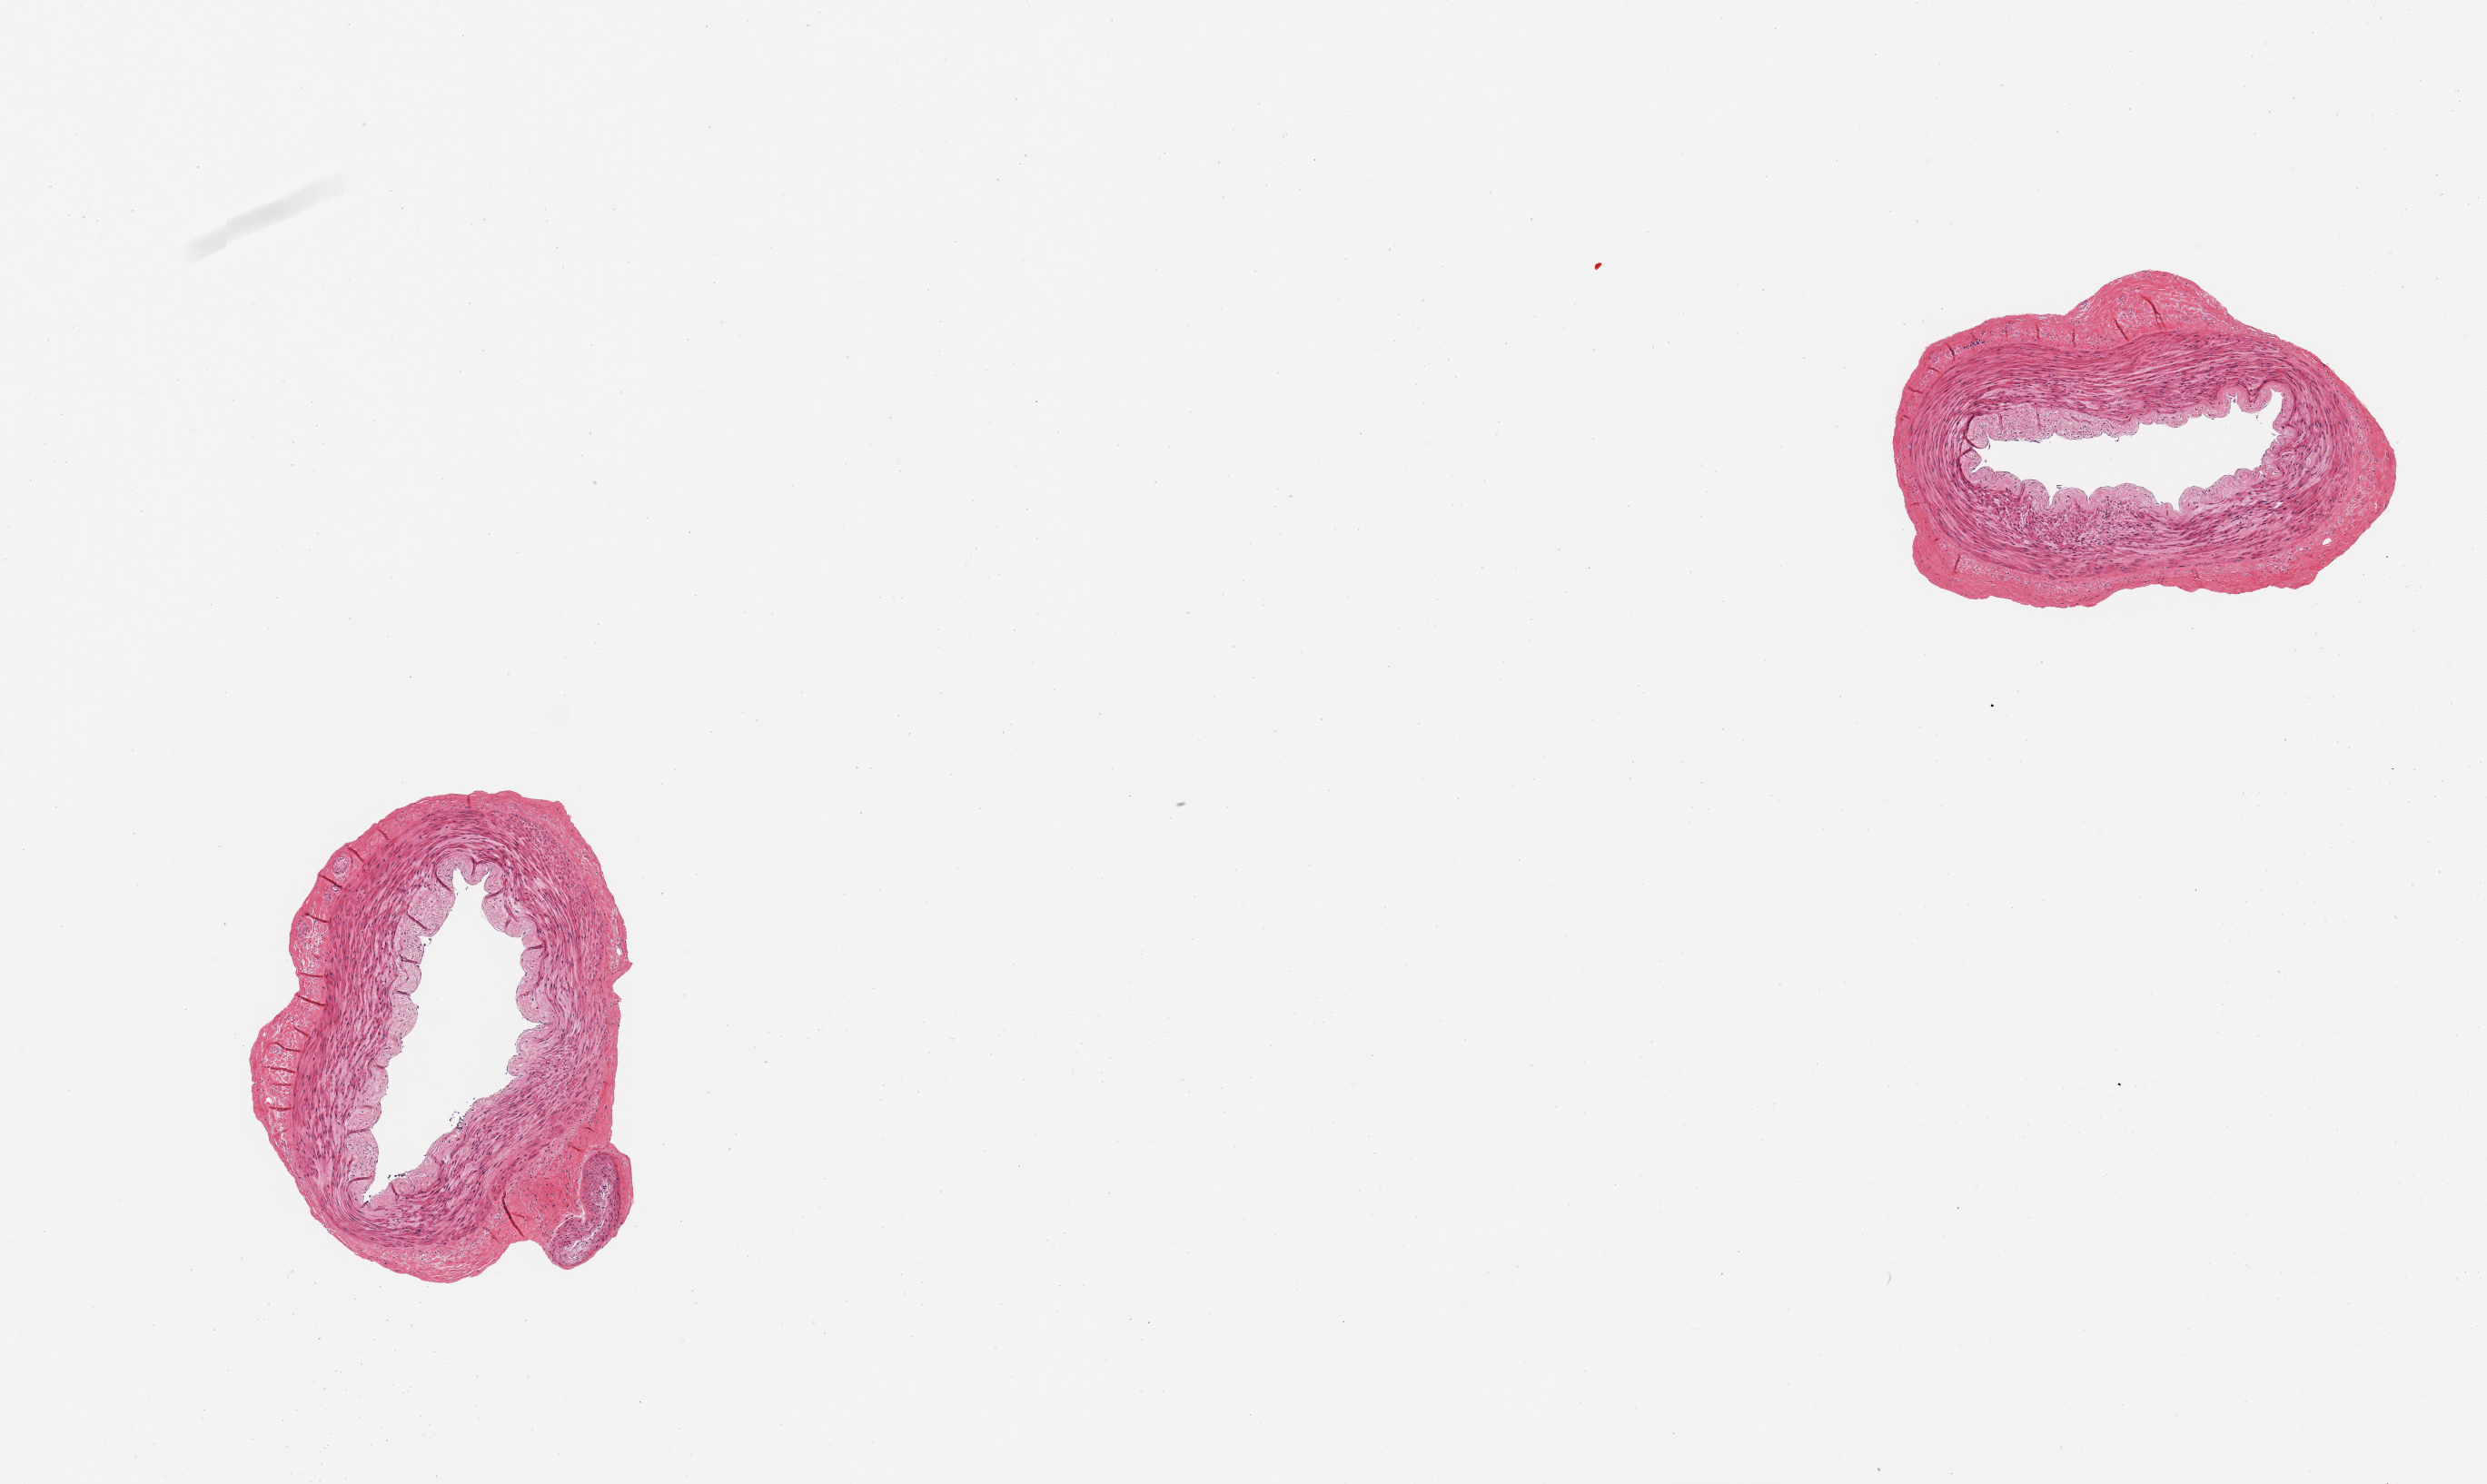
H&E whole-slide image, brightfield, a low-resolution overview of the entire scanned area, about 10.8 x 6.5 mm (from a 20x scan). PAXgene-fixed paraffin-embedded (PFPE) section. Section of tibial artery (target tissue). Tissue donor sample. Female donor.
Review note (as recorded): 2 pieces, no fat or atherosis; good specimens.